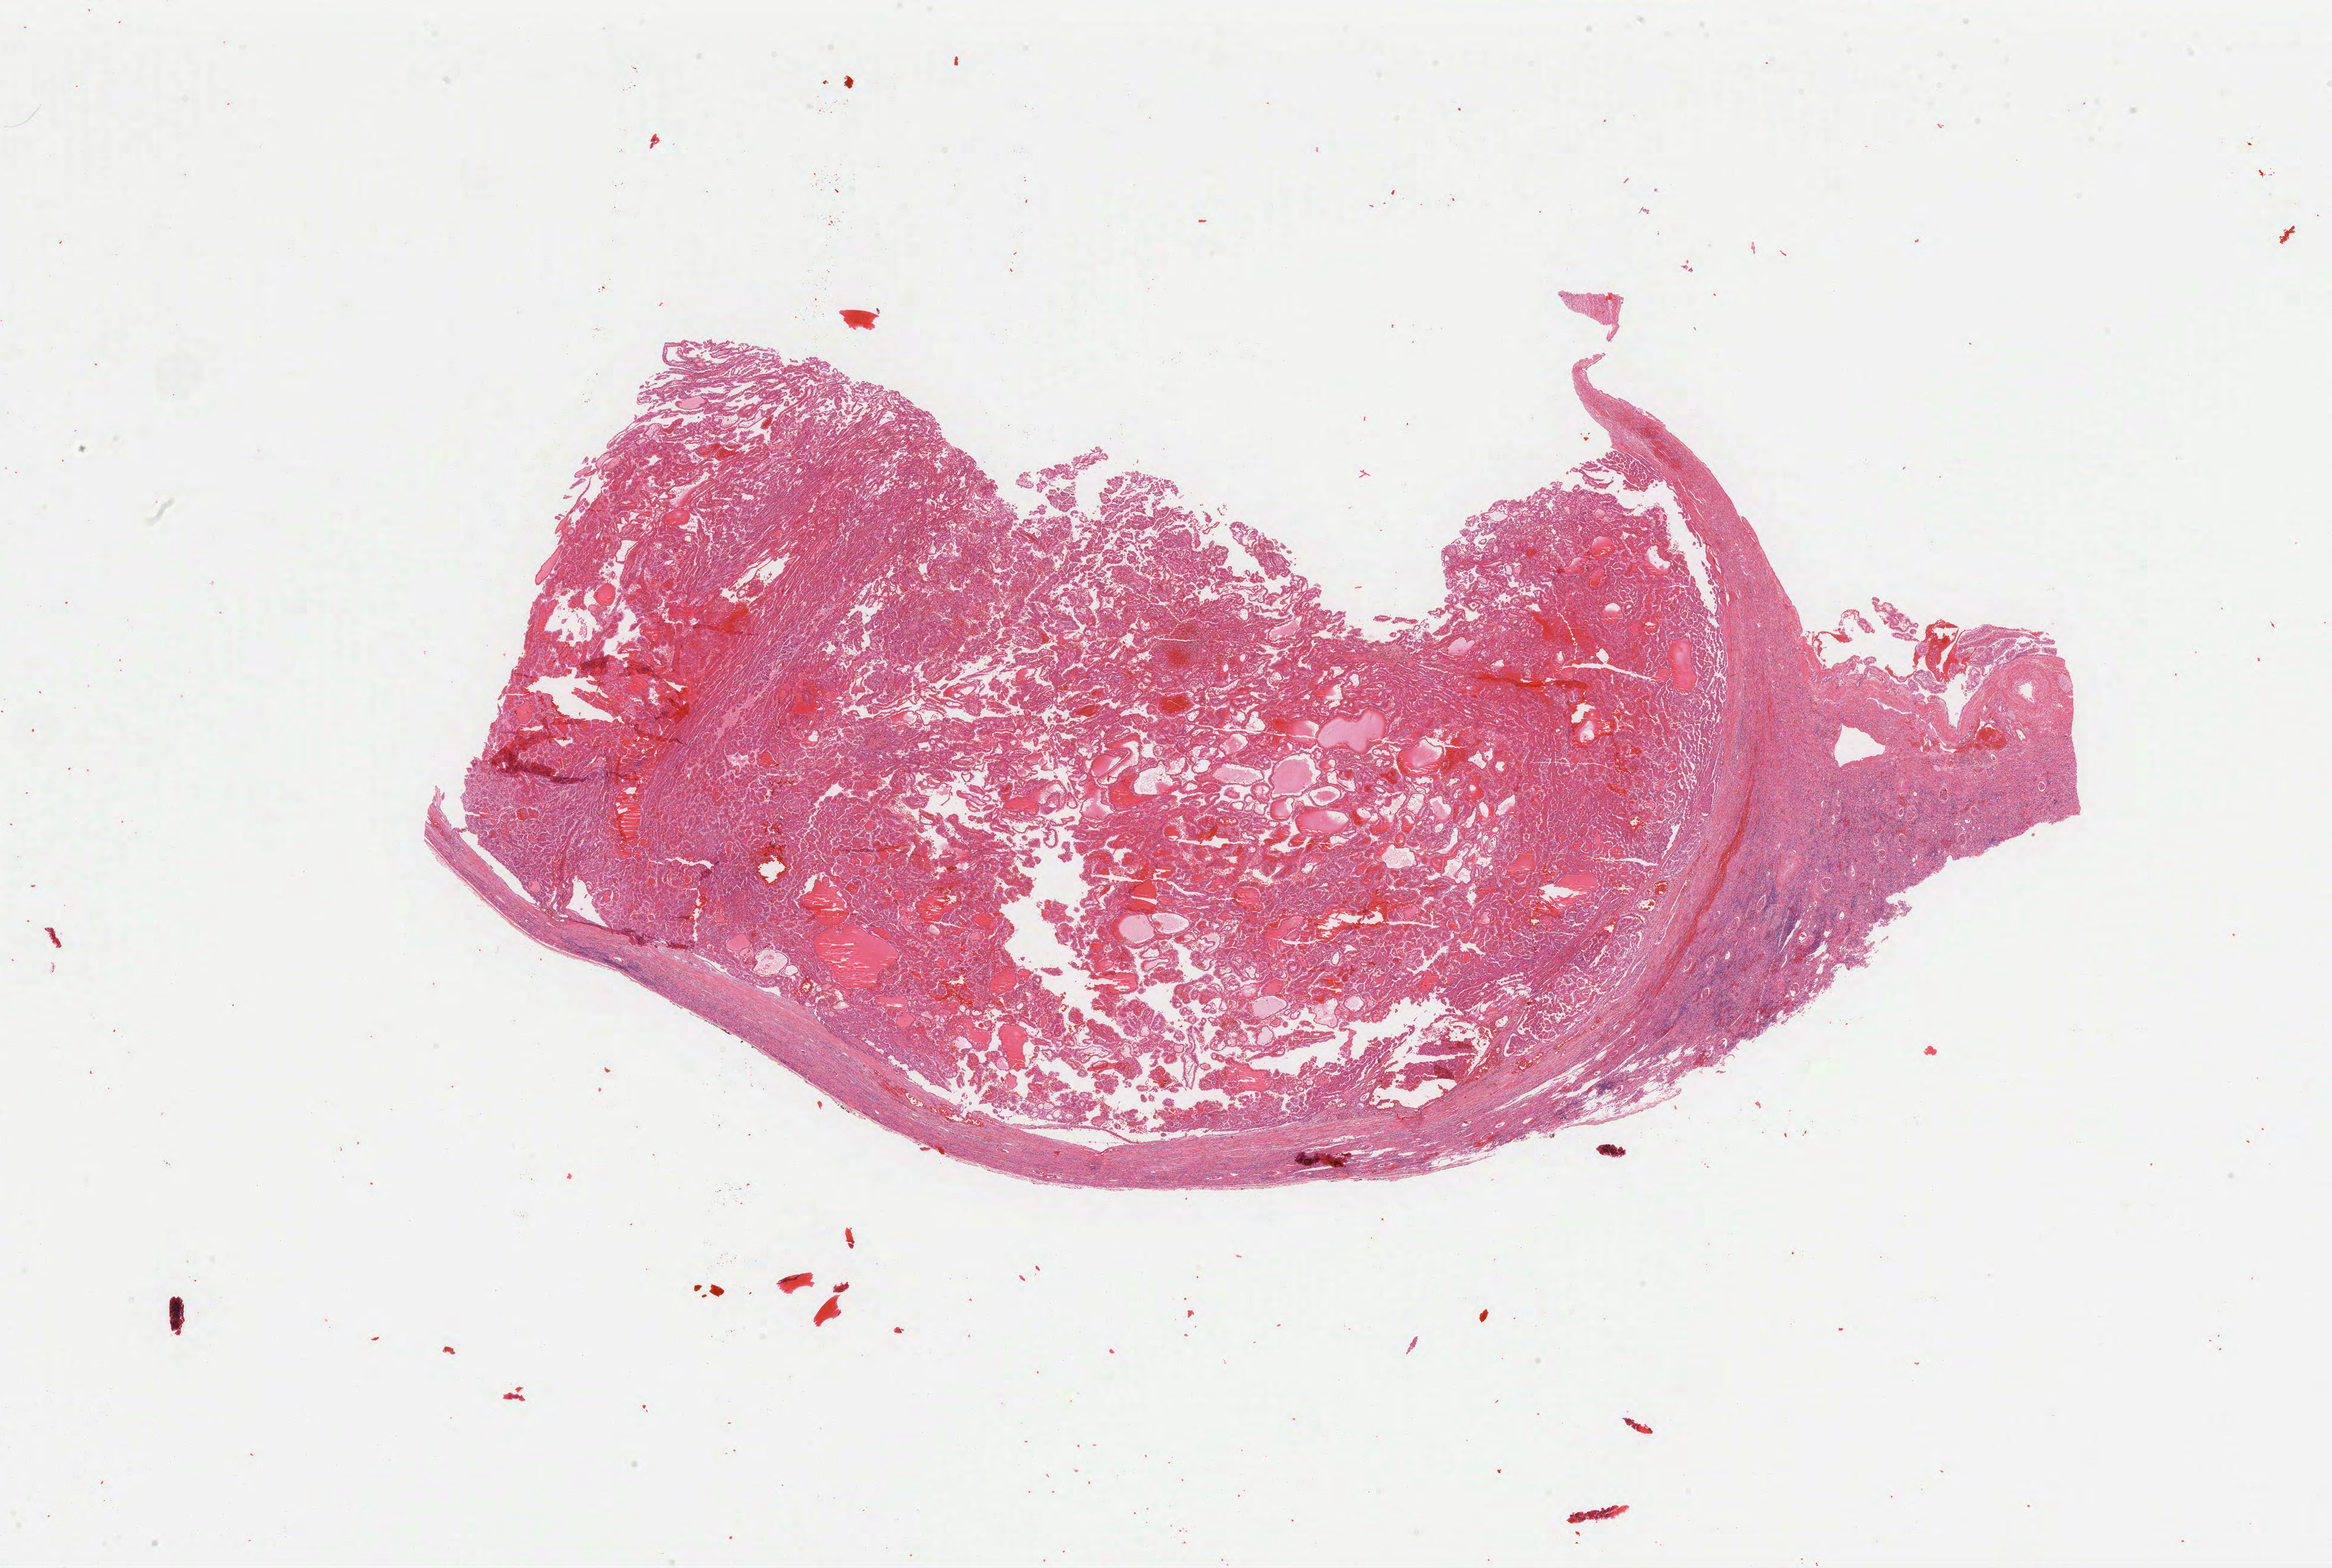
Whole-slide histology image, H&E, whole scanned area (about 30.9 x 20.8 mm, slide scanned at 40x) shown as a low-resolution overview; formalin-fixed paraffin-embedded (FFPE) diagnostic section; primary tumour sample from the kidney. Patient: male, age at initial diagnosis 56 years.
Diagnosis: Papillary adenocarcinoma, NOS. AJCC pathologic stage: III (7th edition). Laterality: left.